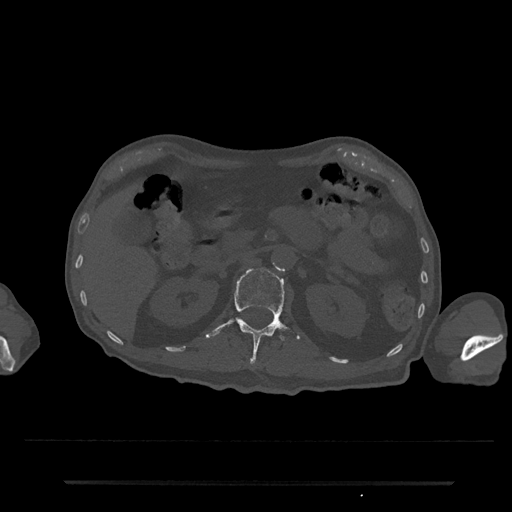
CT including the spine, one axial slice; position 127 of 797 along the scan axis; 120 kVp; bone window (W 1800 / L 400 HU); 0.5 mm slice thickness; 512 × 512 image matrix, field of view 427 × 427 mm. Patient: male, 74 years. Case-level facts recorded for this patient, not image findings: primary cancer: prostate.
Structures marked on this image (semi-automatic segmentation, software-assisted and operator-edited):
- L1 vertebra: box from (x=204, y=268) to (x=300, y=364) px